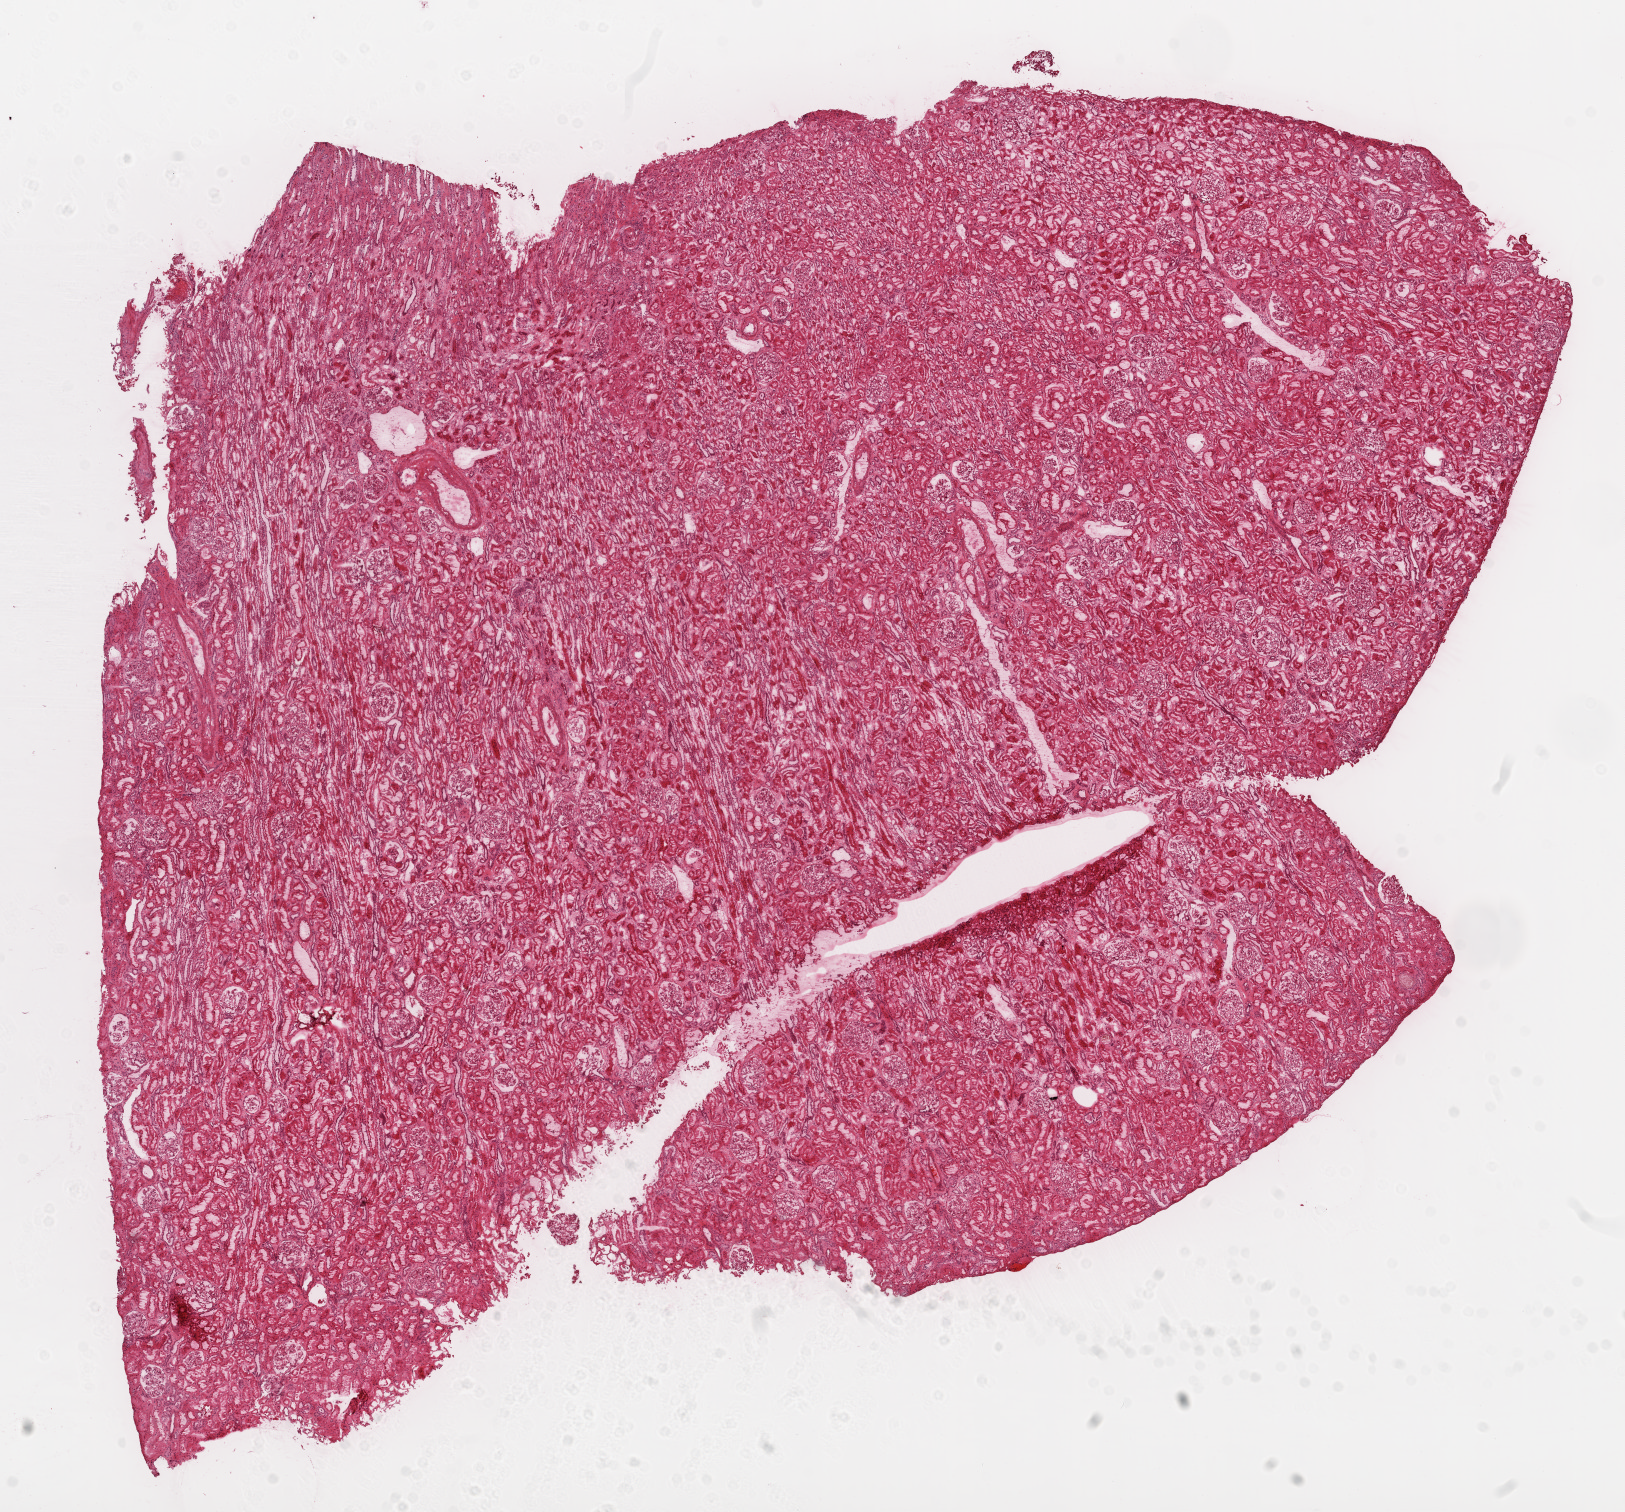
Digitized H&E tissue section (whole slide), shown as a low-resolution overview of the whole scanned area (about 13.0 x 12.1 mm, from a 20x scan), frozen section from the top of the tissue portion, sample: solid tissue normal (non-tumour tissue), kidney. Male patient; age at initial diagnosis 45 years.
This section: solid tissue normal sample (biorepository sample class). Patient diagnosis: Clear cell adenocarcinoma, NOS.